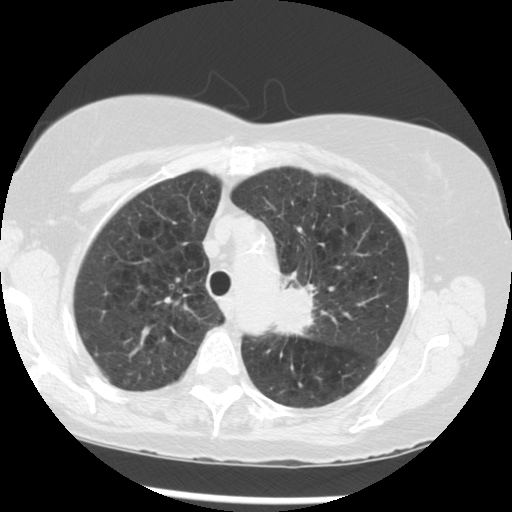
Axial slice from a low-dose chest CT screening exam; third annual screen; lung window (W 1500 / L -600 HU); 2.5 mm slice thickness; standard (soft-tissue) reconstruction kernel (STANDARD); slice 216 of 283 in the series; 512 × 512 image matrix, field of view 330 × 330 mm. Female, age 70 years at enrolment. Current smoker at enrolment.
• Lesion marked by an expert reader, bounding box <265,268,359,358> (left, top, right, bottom; pixels).
• Reader record for this screening exam (exam-level; its link to the box is not recorded): non-calcified nodule or mass ≥4 mm, left upper lobe, 32 × 26 mm, spiculated (stellate) margins, soft tissue attenuation, pre-existing on the prior screen: yes; interval growth: yes.
• Official screen result: positive, other.
• Later outcome: lung cancer diagnosed 24 days after this screen — neoplasm, malignant, left upper lobe, stage IIIB (AJCC 6th edition), 40 mm at pathology.